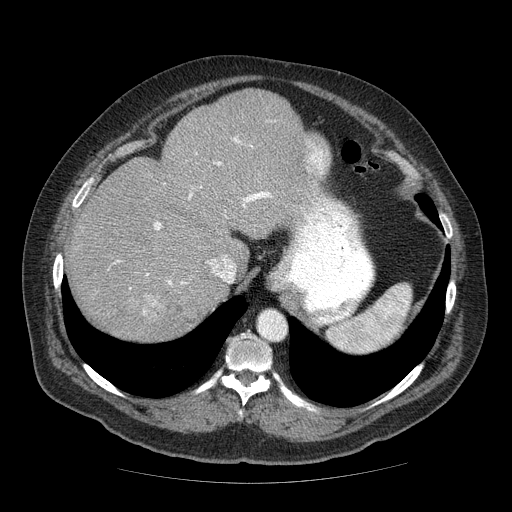
Contrast-enhanced abdominal CT (liver protocol), one axial slice; position 49 of 85 along the scan axis; reconstruction kernel STANDARD; 120 kVp; soft-tissue window (W 400 / L 40 HU); 2.5 mm slice thickness; 512 × 512 image matrix. Case-level facts recorded for this patient, not image findings: diagnosis: hepatocellular carcinoma (patient treated with transarterial chemoembolisation; whether this scan precedes or follows treatment is not stated here); TNM stage (as recorded): Stage-IIIA; Child-Pugh class: A; tumour nodularity: multinodular; tumour size: 7 cm.
Outlined on this slice (semi-automatically segmented with operator editing):
- abdominal aorta: bounding box (x1, y1, x2, y2) in pixels: (258, 310, 286, 340)
- liver parenchyma outside the tumour (the mass and vessels are separate outlines, so this box may not span the whole liver): (66, 90, 324, 341)
- mass: (142, 290, 203, 335)
- liver vessels: (117, 137, 272, 289)